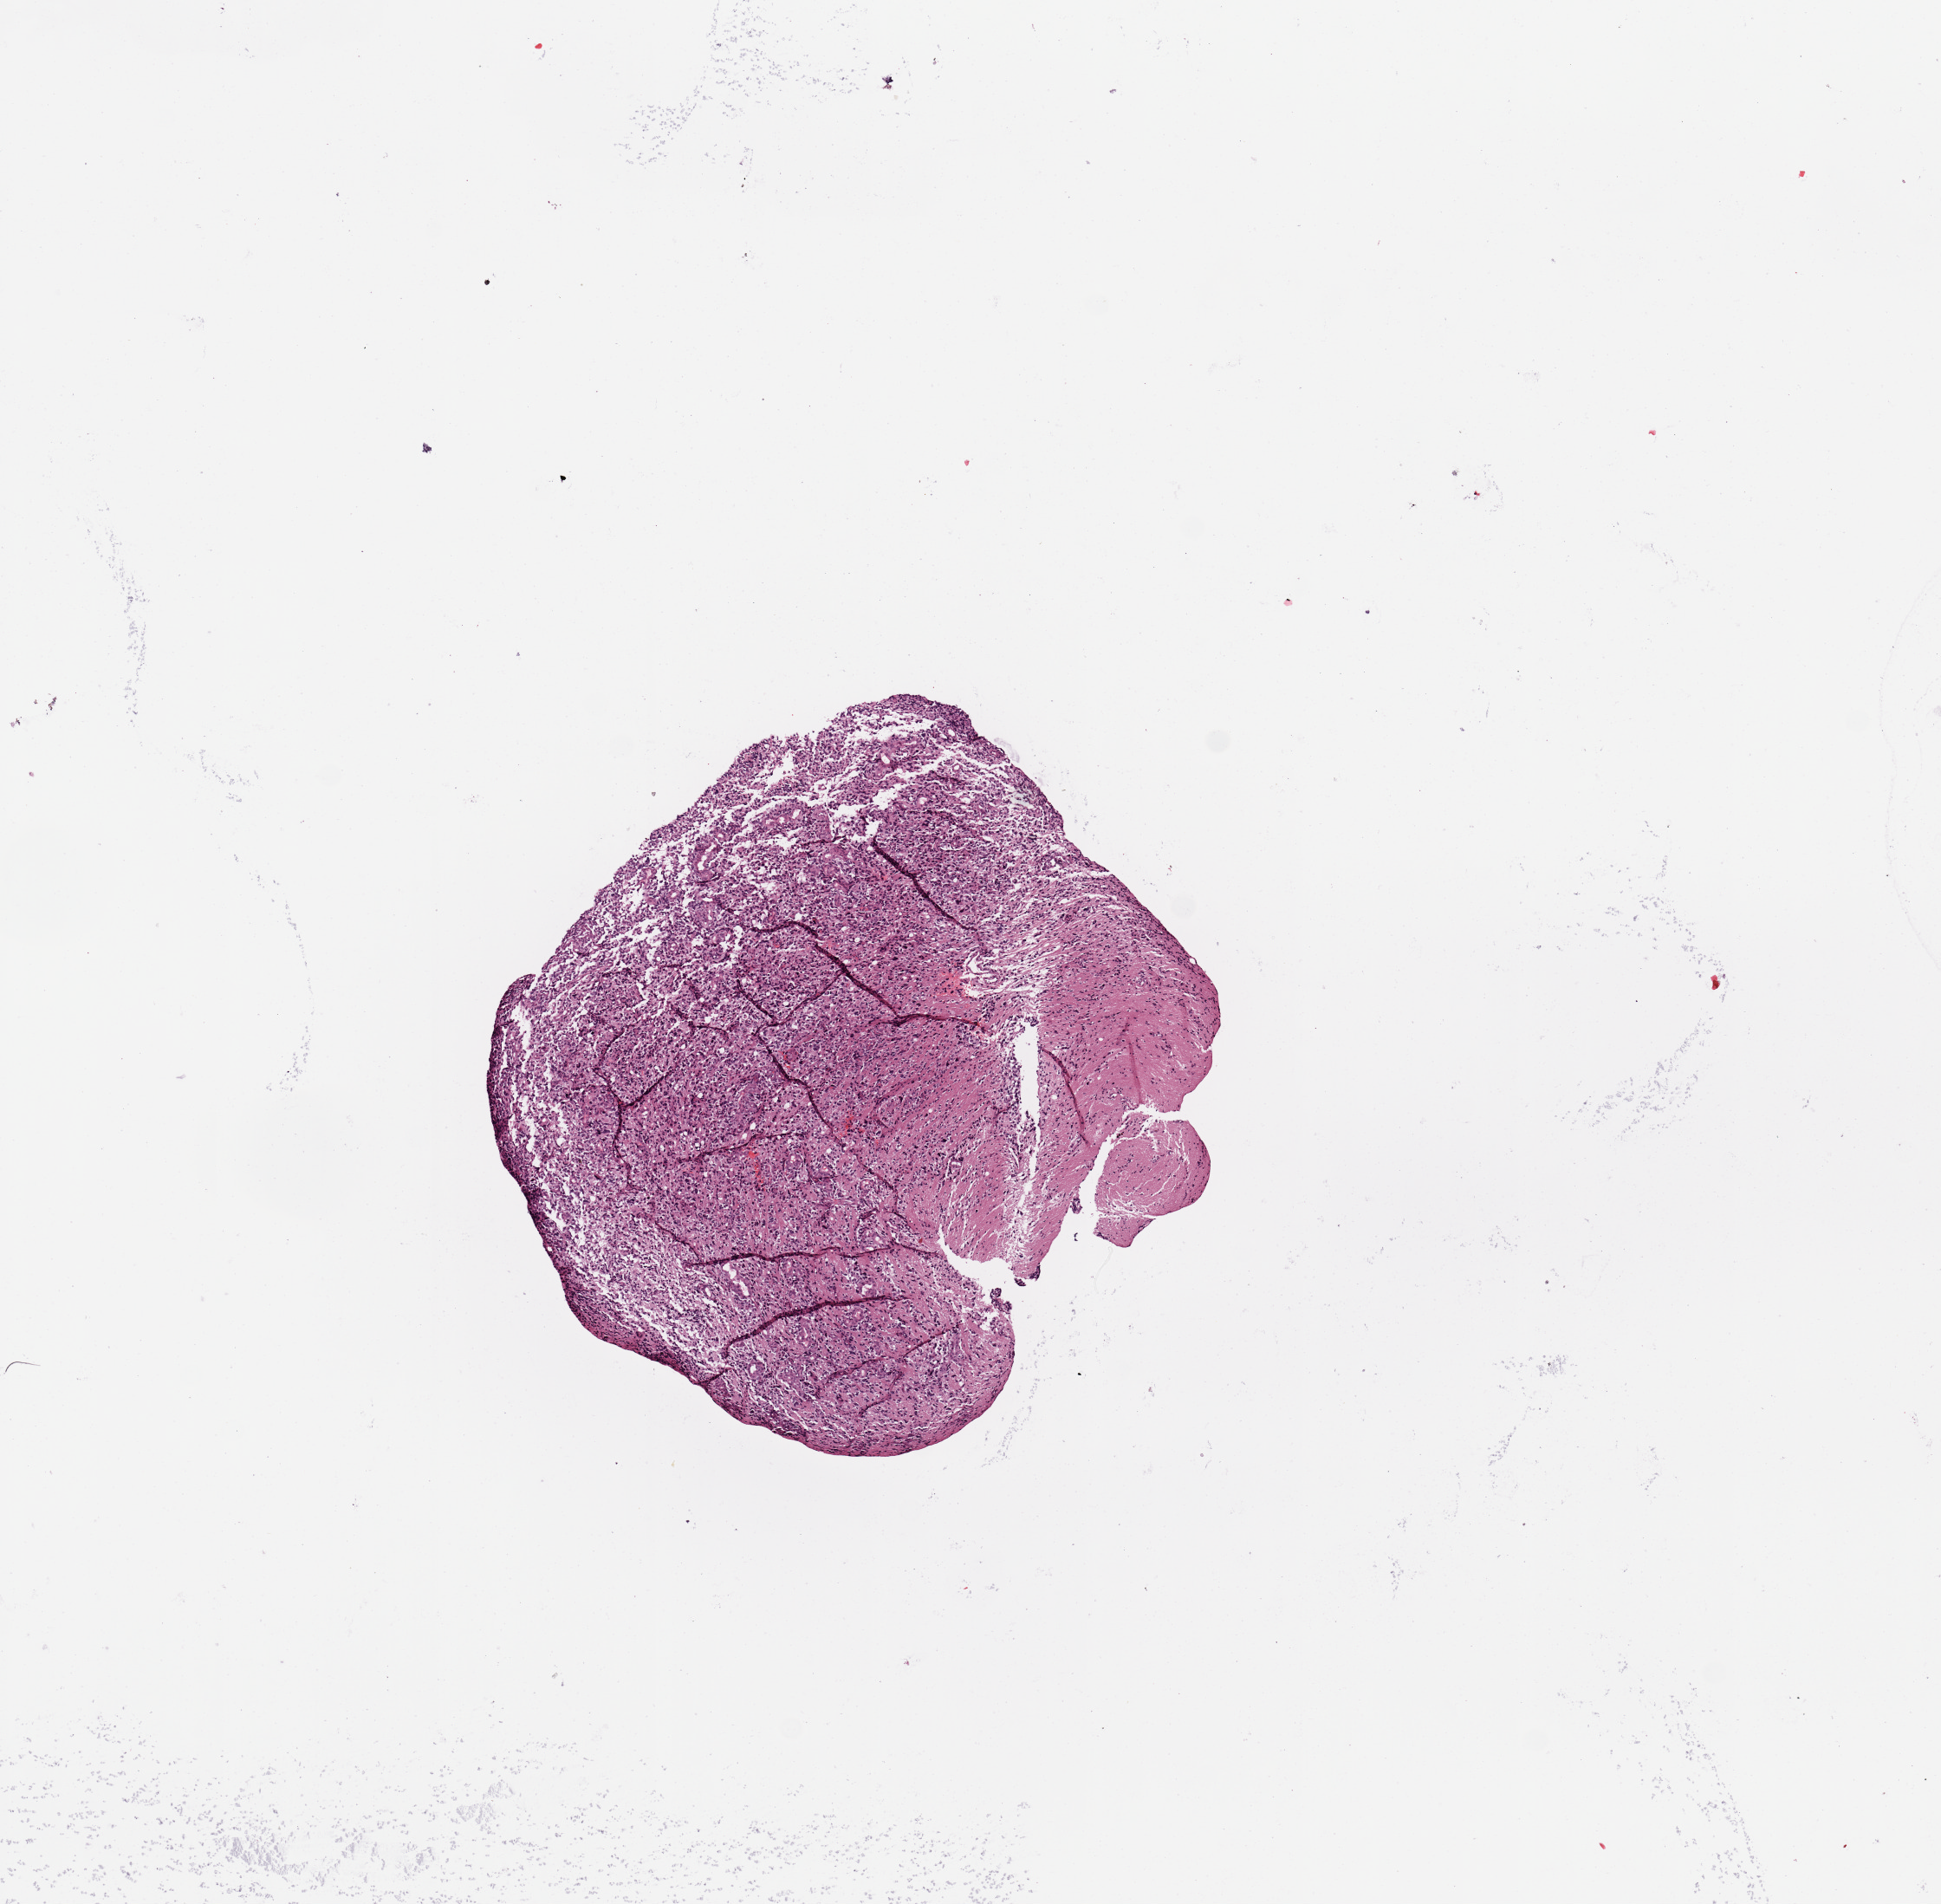
Digitized H&E tissue section (whole slide), whole scanned area (about 8.9 x 8.7 mm) shown as a low-resolution overview. Tumour tissue sample, sampled site: brain. Patient: female, age 30 years. Composition of this section per pathologist review: tumour nuclei 80%, necrosis 5%.
* histologic diagnosis: Glioblastoma